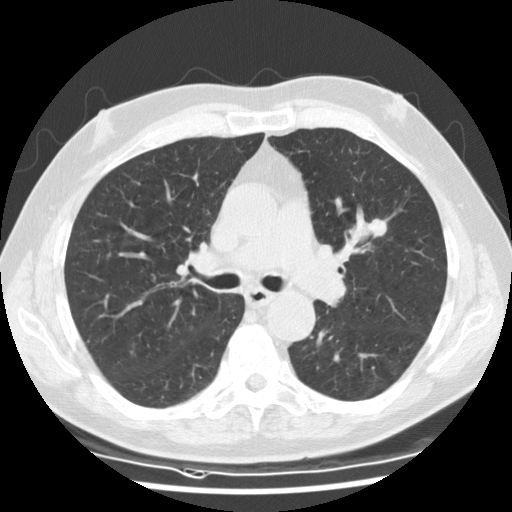
Chest CT (low-dose screening protocol), one axial image. Baseline annual screen. Lung window (W 1500 / L -600 HU). Standard (soft-tissue) reconstruction kernel (STANDARD). 120 kVp. Slice 58 of 135 in the series. 512 × 512 image matrix. Male participant, aged 73 years at enrolment.
• Expert reader's lesion annotation, box from (x=343, y=202) to (x=406, y=254) px.
• The exam's reader record, not a measurement of the box and not confirmed to be the same lesion: non-calcified nodule or mass ≥4 mm, right lower lobe, 13 × 13 mm, smooth margins, soft tissue attenuation.
• Note: the box lies in the patient's left hemithorax on this image, whereas the reader's record names the right lung; they may be different findings.